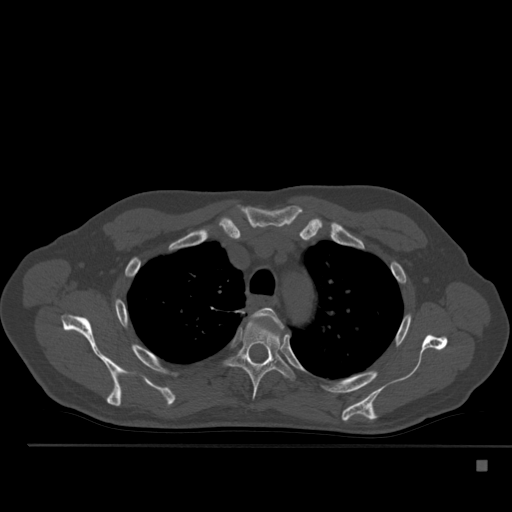
CT including the spine, one axial slice; position 384 of 517 along the scan axis; reconstruction kernel Br40s; bone window (W 1800 / L 400 HU); 1.5 mm slice thickness; 512 × 512 image matrix. Male patient, age 70 years. From the clinical record (not read from this slice): primary cancer: renal; vertebrae with lytic lesions (as recorded): T4, T6, T10, T12, L3, L4, L5.
Annotated regions visible in this slice (semi-automatically segmented with operator editing):
- T3 vertebra: bounding box (x1, y1, x2, y2) in pixels: (253, 307, 283, 329)
- T4 vertebra: (226, 320, 295, 400)